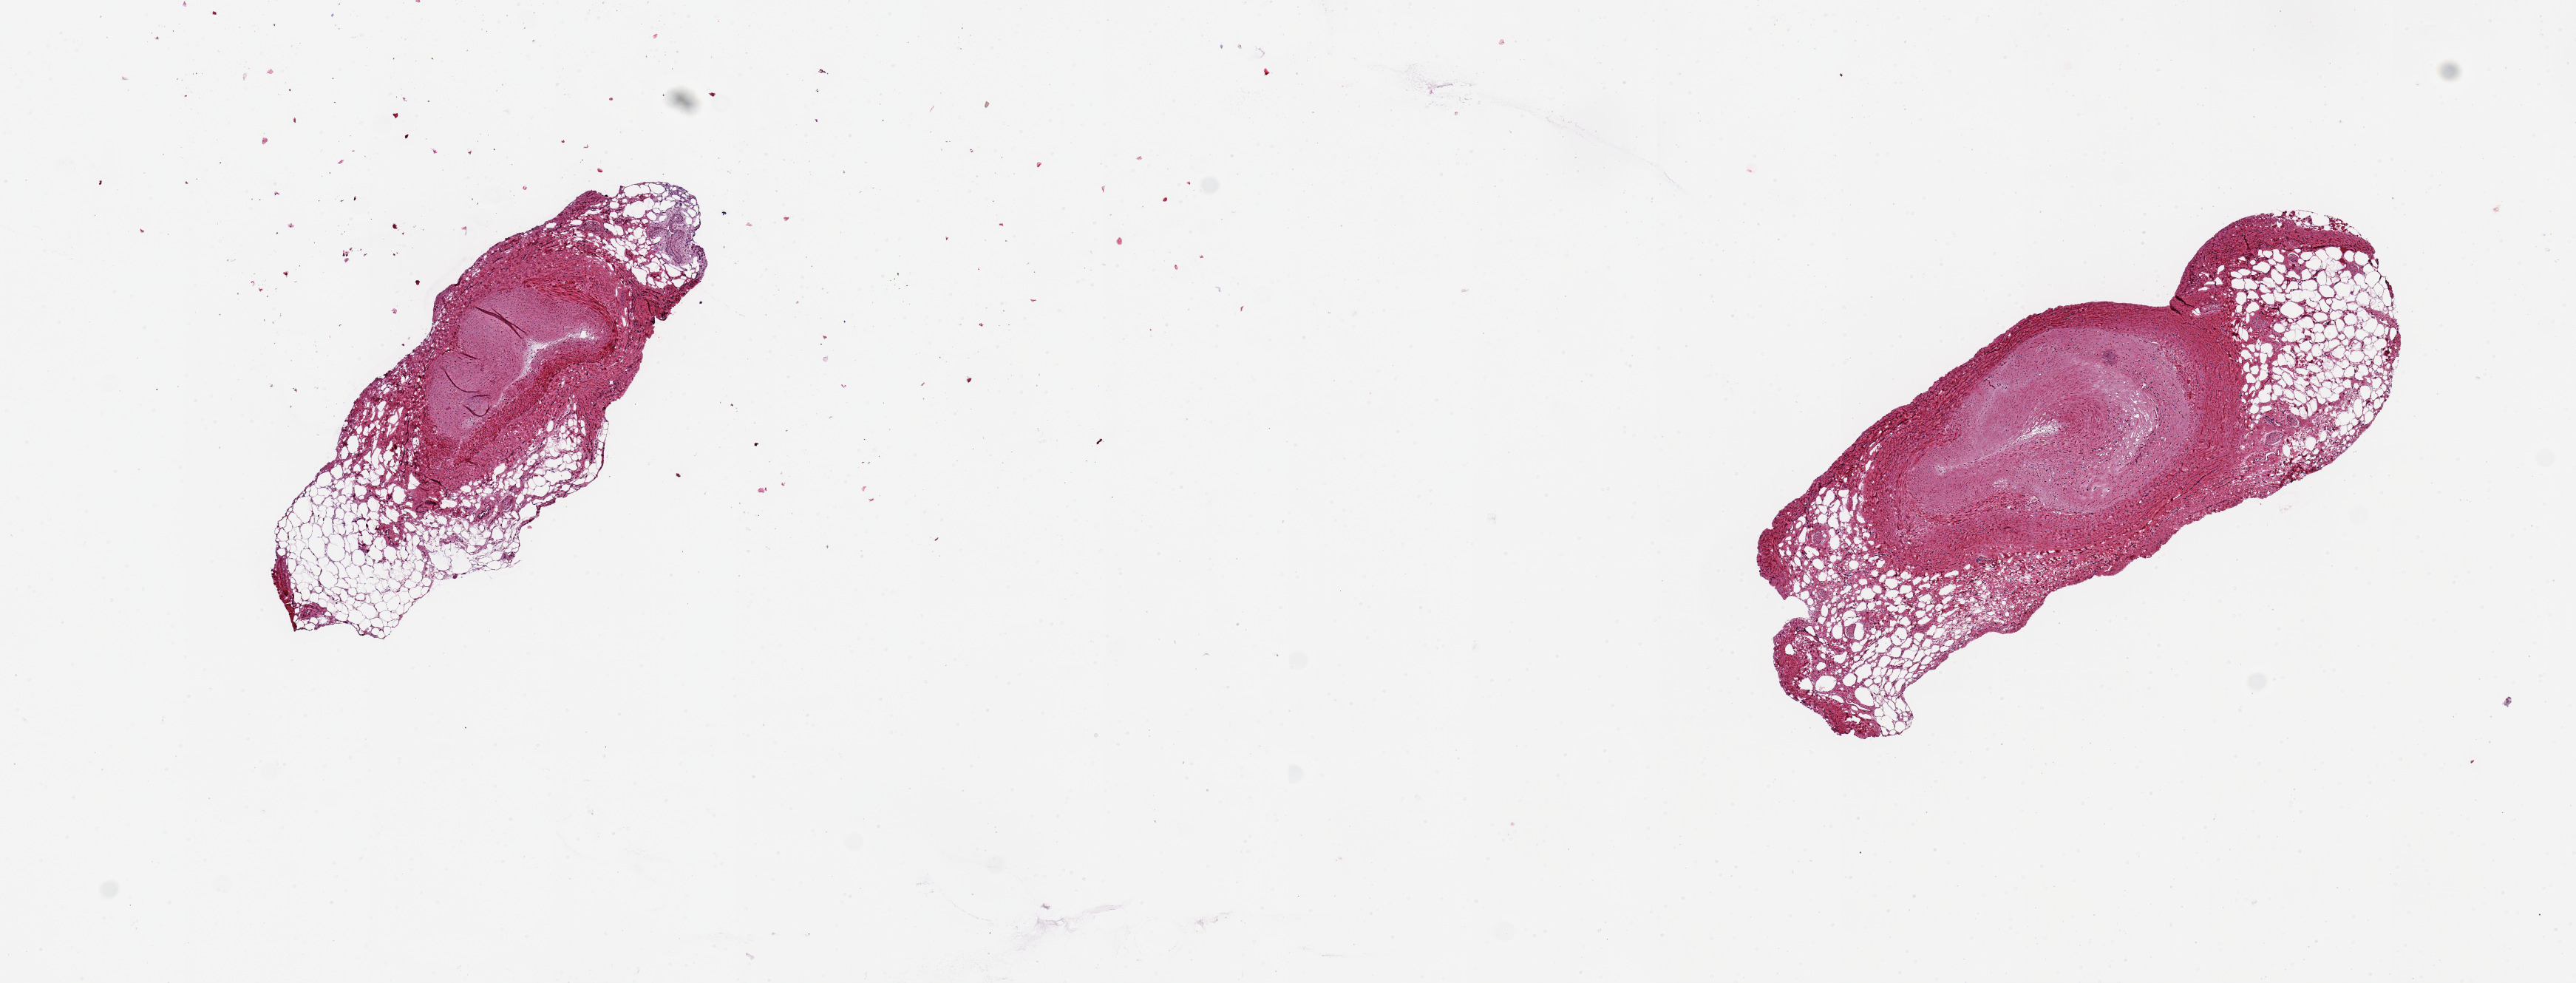
Digitized H&E-stained section, low-resolution overview of the scanned area, about 13.8 x 5.3 mm. PAXgene-fixed, paraffin-embedded tissue. Section of coronary artery (target tissue). Donor tissue sample.
Reviewer comment on this tissue sample: 2 pieces. 3x2 7 4x2mm; 2 mm artery severely occluded by atheromatous plaque; 1 mm untrimmed adipose at each end.